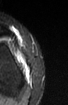
MRI of an extremity soft-tissue mass, one axial slice. Position 20 of 52 along the scan axis. STIR. MR volume resampled by the dataset authors to the PET/CT grid (not the native acquisition matrix). 3.27 mm slice thickness. 68 × 105 image matrix. Female patient. From the clinical record (not read from this slice): histological type: spindle cell suggestive of biphasic synovial sarcoma; grade: intermediate; site of the primary tumour: left knee.
Outlined on this slice (expert contour drawn on MRI and transferred to this co-registered scan by the dataset authors):
- gross tumour volume including surrounding oedema: bounding box (x1, y1, x2, y2) in pixels: (17, 54, 29, 76)
- gross tumour volume (mass): (17, 54, 29, 74)